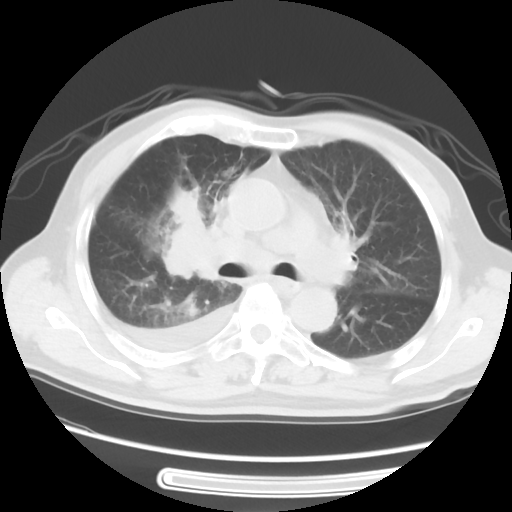
Chest CT, one axial slice. Position 34 of 56 along the scan axis. Lung window (W 1500 / L -600 HU). 5 mm slice thickness. 512 × 512 image matrix, field of view 360 × 360 mm. Patient: male, 77 years. From the clinical record (not read from this slice): clinical TNM (as recorded): T3 N3 M1b; histopathological grade: G3.
Annotated regions visible in this slice (rectangle marked by the reading radiologist):
- lung tumour (recorded histology: small cell carcinoma): box from (x=154, y=183) to (x=223, y=289) px